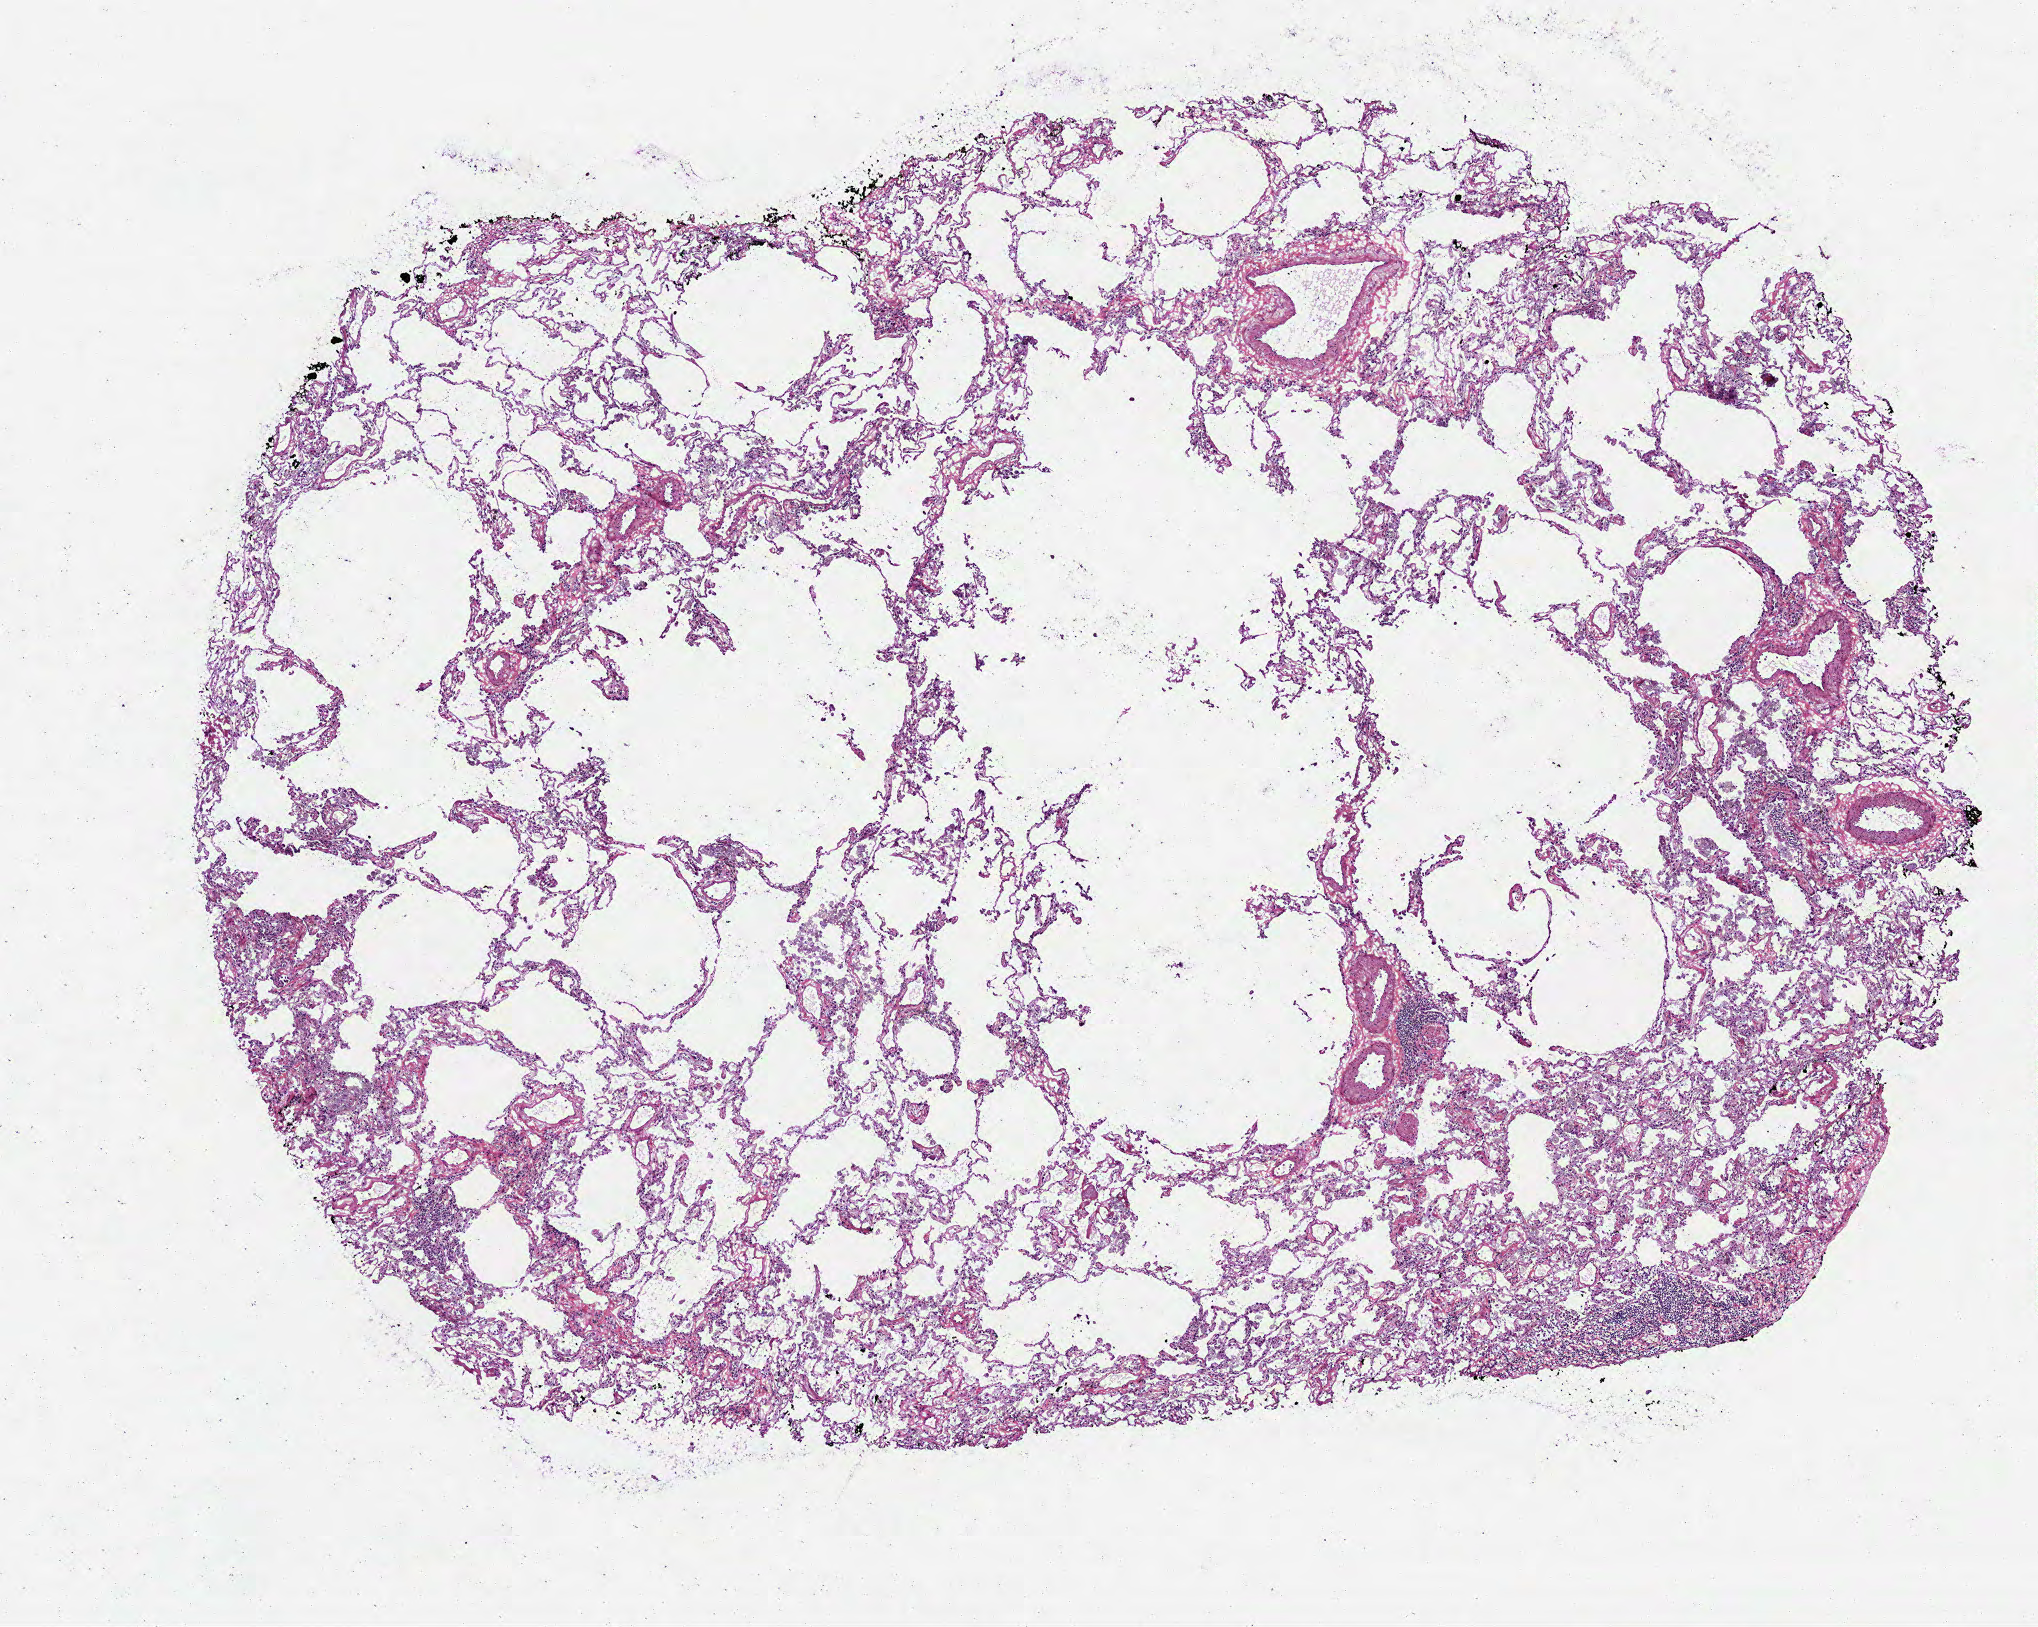
Digitized Hematoxylin and eosin (H&E) stained tissue section (whole slide), a low-resolution overview of the entire scanned area, about 8.2 x 6.6 mm, frozen section from the top of the tissue portion, solid tissue normal (non-tumour tissue) sample from the lung. Patient: female, age at initial diagnosis 71 years.
This section: solid tissue normal sample (biorepository sample class). Patient diagnosis: Adenocarcinoma, NOS (upper lobe, lung).